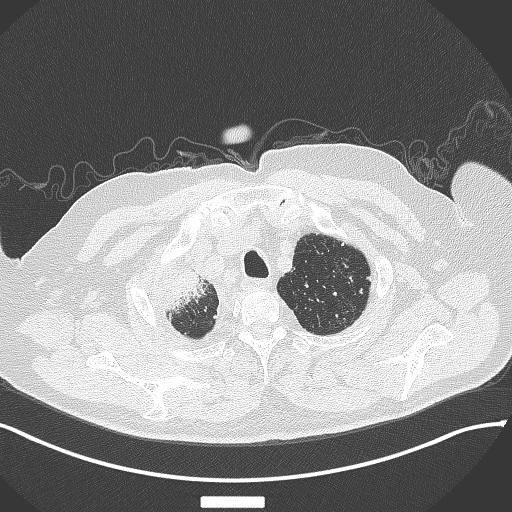
Chest CT, one axial slice; position 327 of 384 along the scan axis; reconstruction kernel B70f; lung window (W 1500 / L -600 HU); 512 × 512 image matrix, field of view 400 × 400 mm. Patient: male, 69 years. Case-level facts recorded for this patient, not image findings: clinical TNM (as recorded): T4 N3 M1.
Annotated regions visible in this slice (rectangle marked by the reading radiologist):
- lung tumour (recorded histology: adenocarcinoma): box from (x=156, y=260) to (x=208, y=316) px